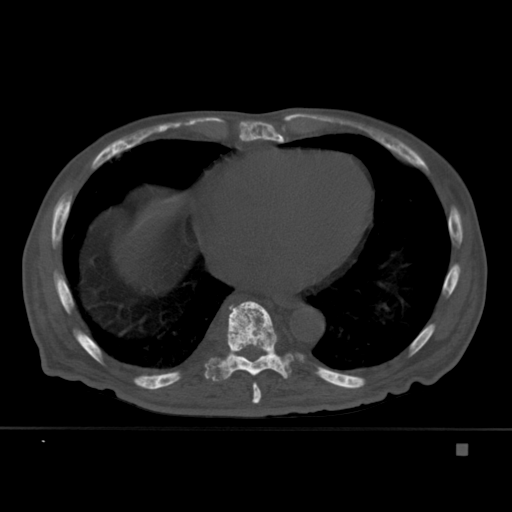
CT including the spine, one axial slice. Slice 249 of 451 in the series (ordered by position). Bone window (W 1800 / L 400 HU). 1.5 mm slice thickness. 512 × 512 image matrix, field of view 378 × 378 mm. Patient: male, 75 years. From the clinical record (not read from this slice): primary cancer: prostate.
Structures marked on this image (semi-automatically segmented with operator editing):
- T10 vertebra: box from (x=237, y=353) to (x=277, y=356) px
- T8 vertebra: (x=250, y=373)–(x=262, y=404)
- T9 vertebra: (x=204, y=301)–(x=294, y=381)